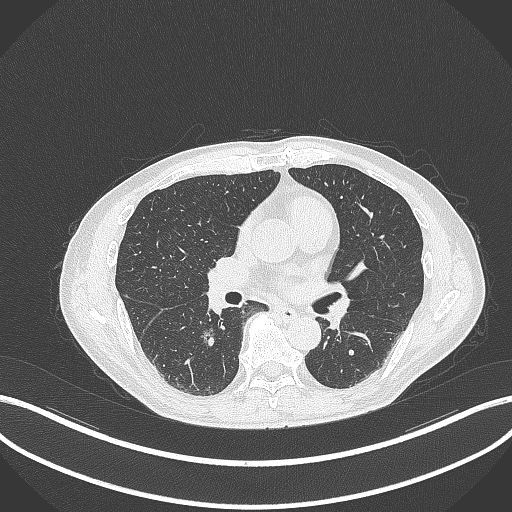
Chest CT, one axial slice. Position 166 of 323 along the scan axis. Lung window (W 1500 / L -600 HU). 512 × 512 image matrix. Patient: male, 61 years. Case-level facts recorded for this patient, not image findings: clinical TNM (as recorded): T1c N0 M0.
Structures marked on this image (rectangle marked by the reading radiologist):
- lung tumour (recorded histology: adenocarcinoma): bounding box <202,328,221,346> (left, top, right, bottom; pixels)